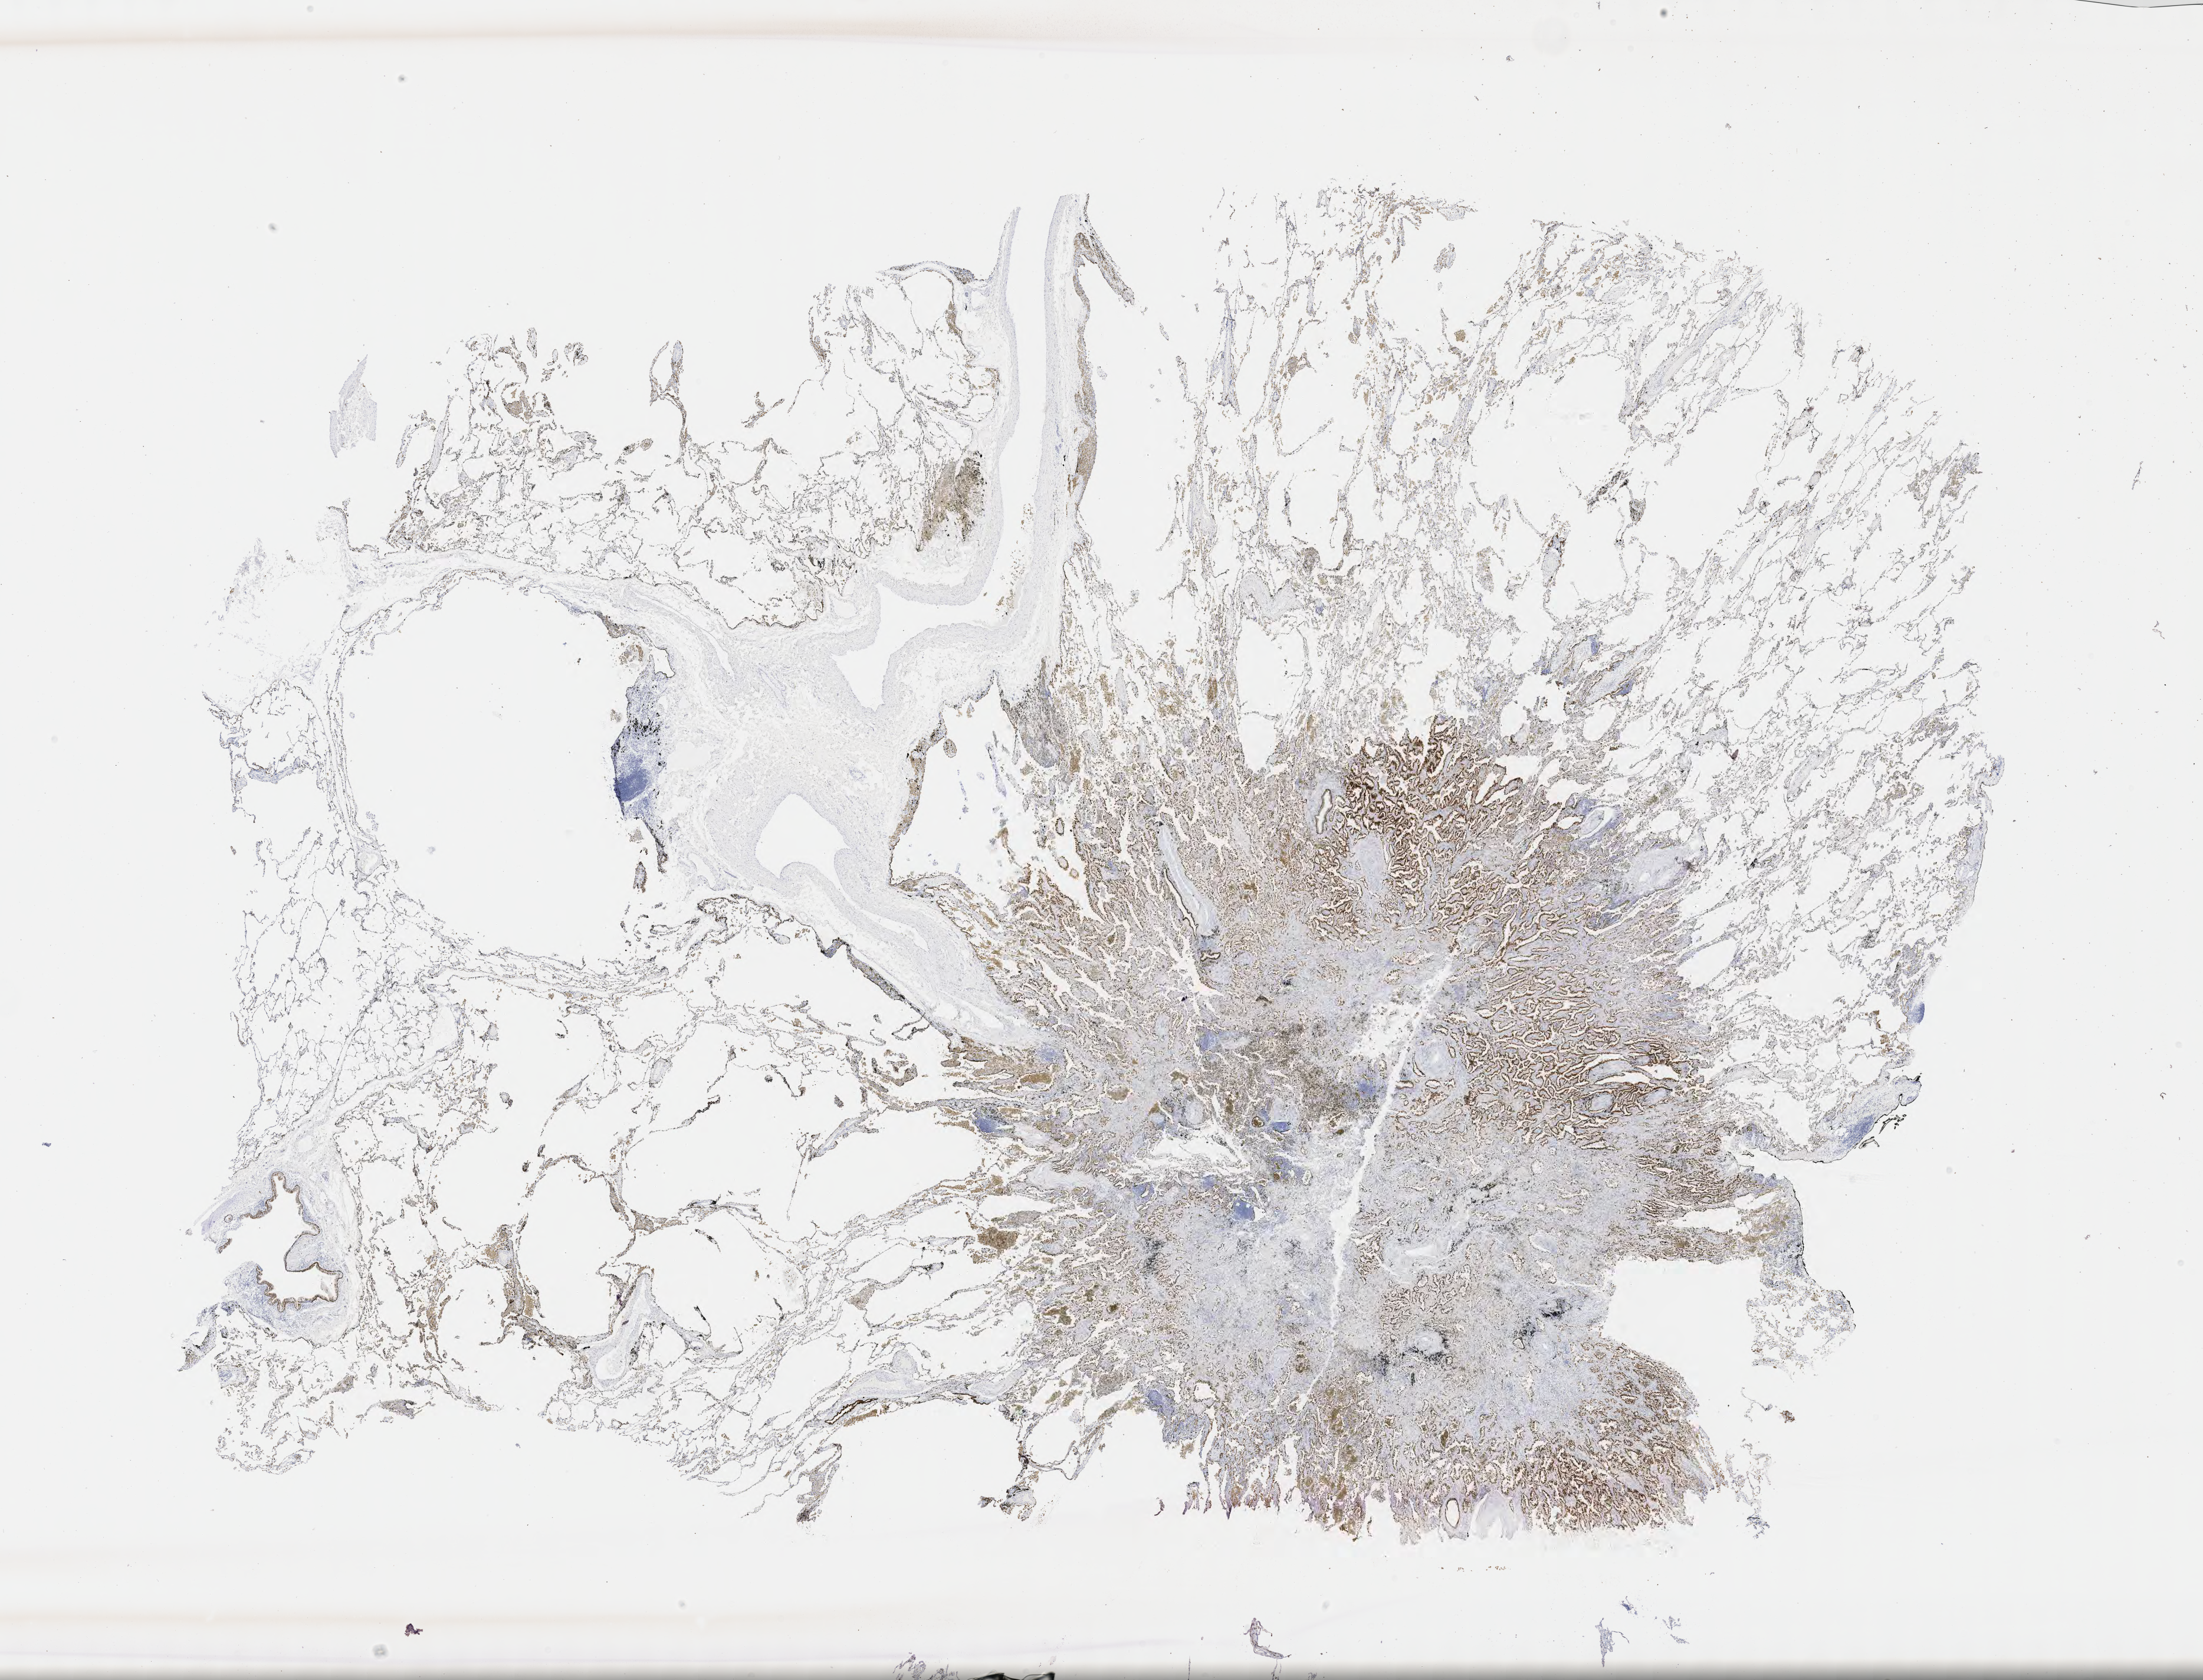
IHC for TTF-1 (thyroid transcription factor 1), whole-slide image — whole scanned area (about 30.2 x 23.0 mm) shown as a low-resolution overview; specimen: tumor tissue; anatomic site: lung. Patient sex: male.
Diagnosis: Mucinous adenocarcinoma.